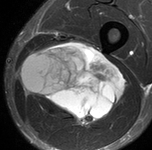
MRI of an extremity soft-tissue mass, one axial slice. Position 51 of 90 along the scan axis. STIR. MR volume resampled by the dataset authors to the PET/CT grid (not the native acquisition matrix). 152 × 150 image matrix, field of view 148 × 146 mm. Male patient. From the clinical record (not read from this slice): histological type: undifferentiated pleomorphic liposarcoma; grade: high; site of the primary tumour: left thigh.
Outlined on this slice (expert contour drawn on MRI and transferred to this co-registered scan by the dataset authors):
- gross tumour volume including surrounding oedema: bounding box <18,41,128,127> (left, top, right, bottom; pixels)
- gross tumour volume (mass): <20,41,128,127>